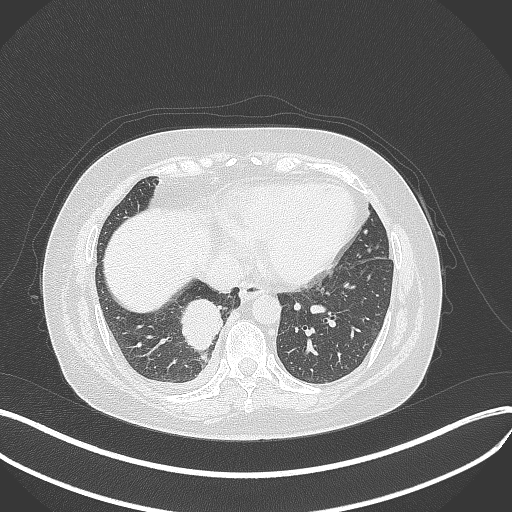
Chest CT, one axial slice. Position 111 of 381 along the scan axis. Reconstruction kernel B70f. 120 kVp. Lung window (W 1500 / L -600 HU). 512 × 512 image matrix, field of view 400 × 400 mm. Female patient, age 56 years. From the clinical record (not read from this slice): clinical TNM (as recorded): T2b N1 M0; histopathological grade: G3.
Structures marked on this image (bounding box drawn by a radiologist):
- lung tumour (recorded histology: small cell carcinoma): bounding box <176,294,223,353> (left, top, right, bottom; pixels)